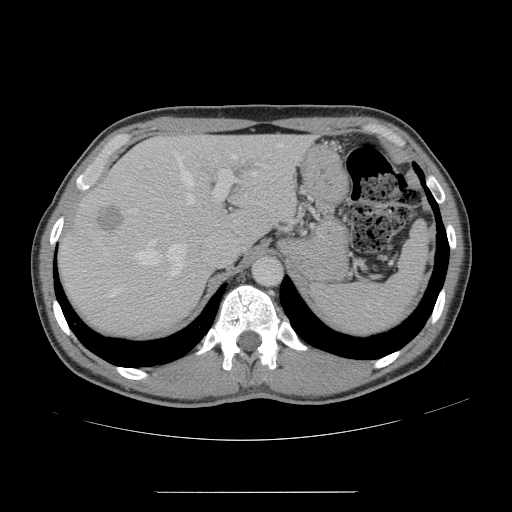
Contrast-enhanced abdominal CT, one axial slice. Slice 111 of 178 in the series (ordered by position). 120 kVp. Intravenous contrast given. Soft-tissue window (W 400 / L 40 HU). 512 × 512 image matrix, field of view 401 × 401 mm. Male patient, age 53 years. Case-level facts recorded for this patient, not image findings: diagnosis: colorectal cancer liver metastases, imaged before liver resection; multiple liver metastases: yes; largest metastasis: 2.4 cm.
Structures marked on this image (outlined manually by an expert reader):
- hepatic veins: bounding box (x1, y1, x2, y2) in pixels: (109, 143, 282, 297)
- liver: (61, 136, 308, 335)
- planned liver remnant (the part of the liver to remain after resection): (147, 136, 308, 244)
- portal vein (with intrahepatic branches): (130, 155, 268, 214)
- liver metastasis: (98, 207, 125, 233)